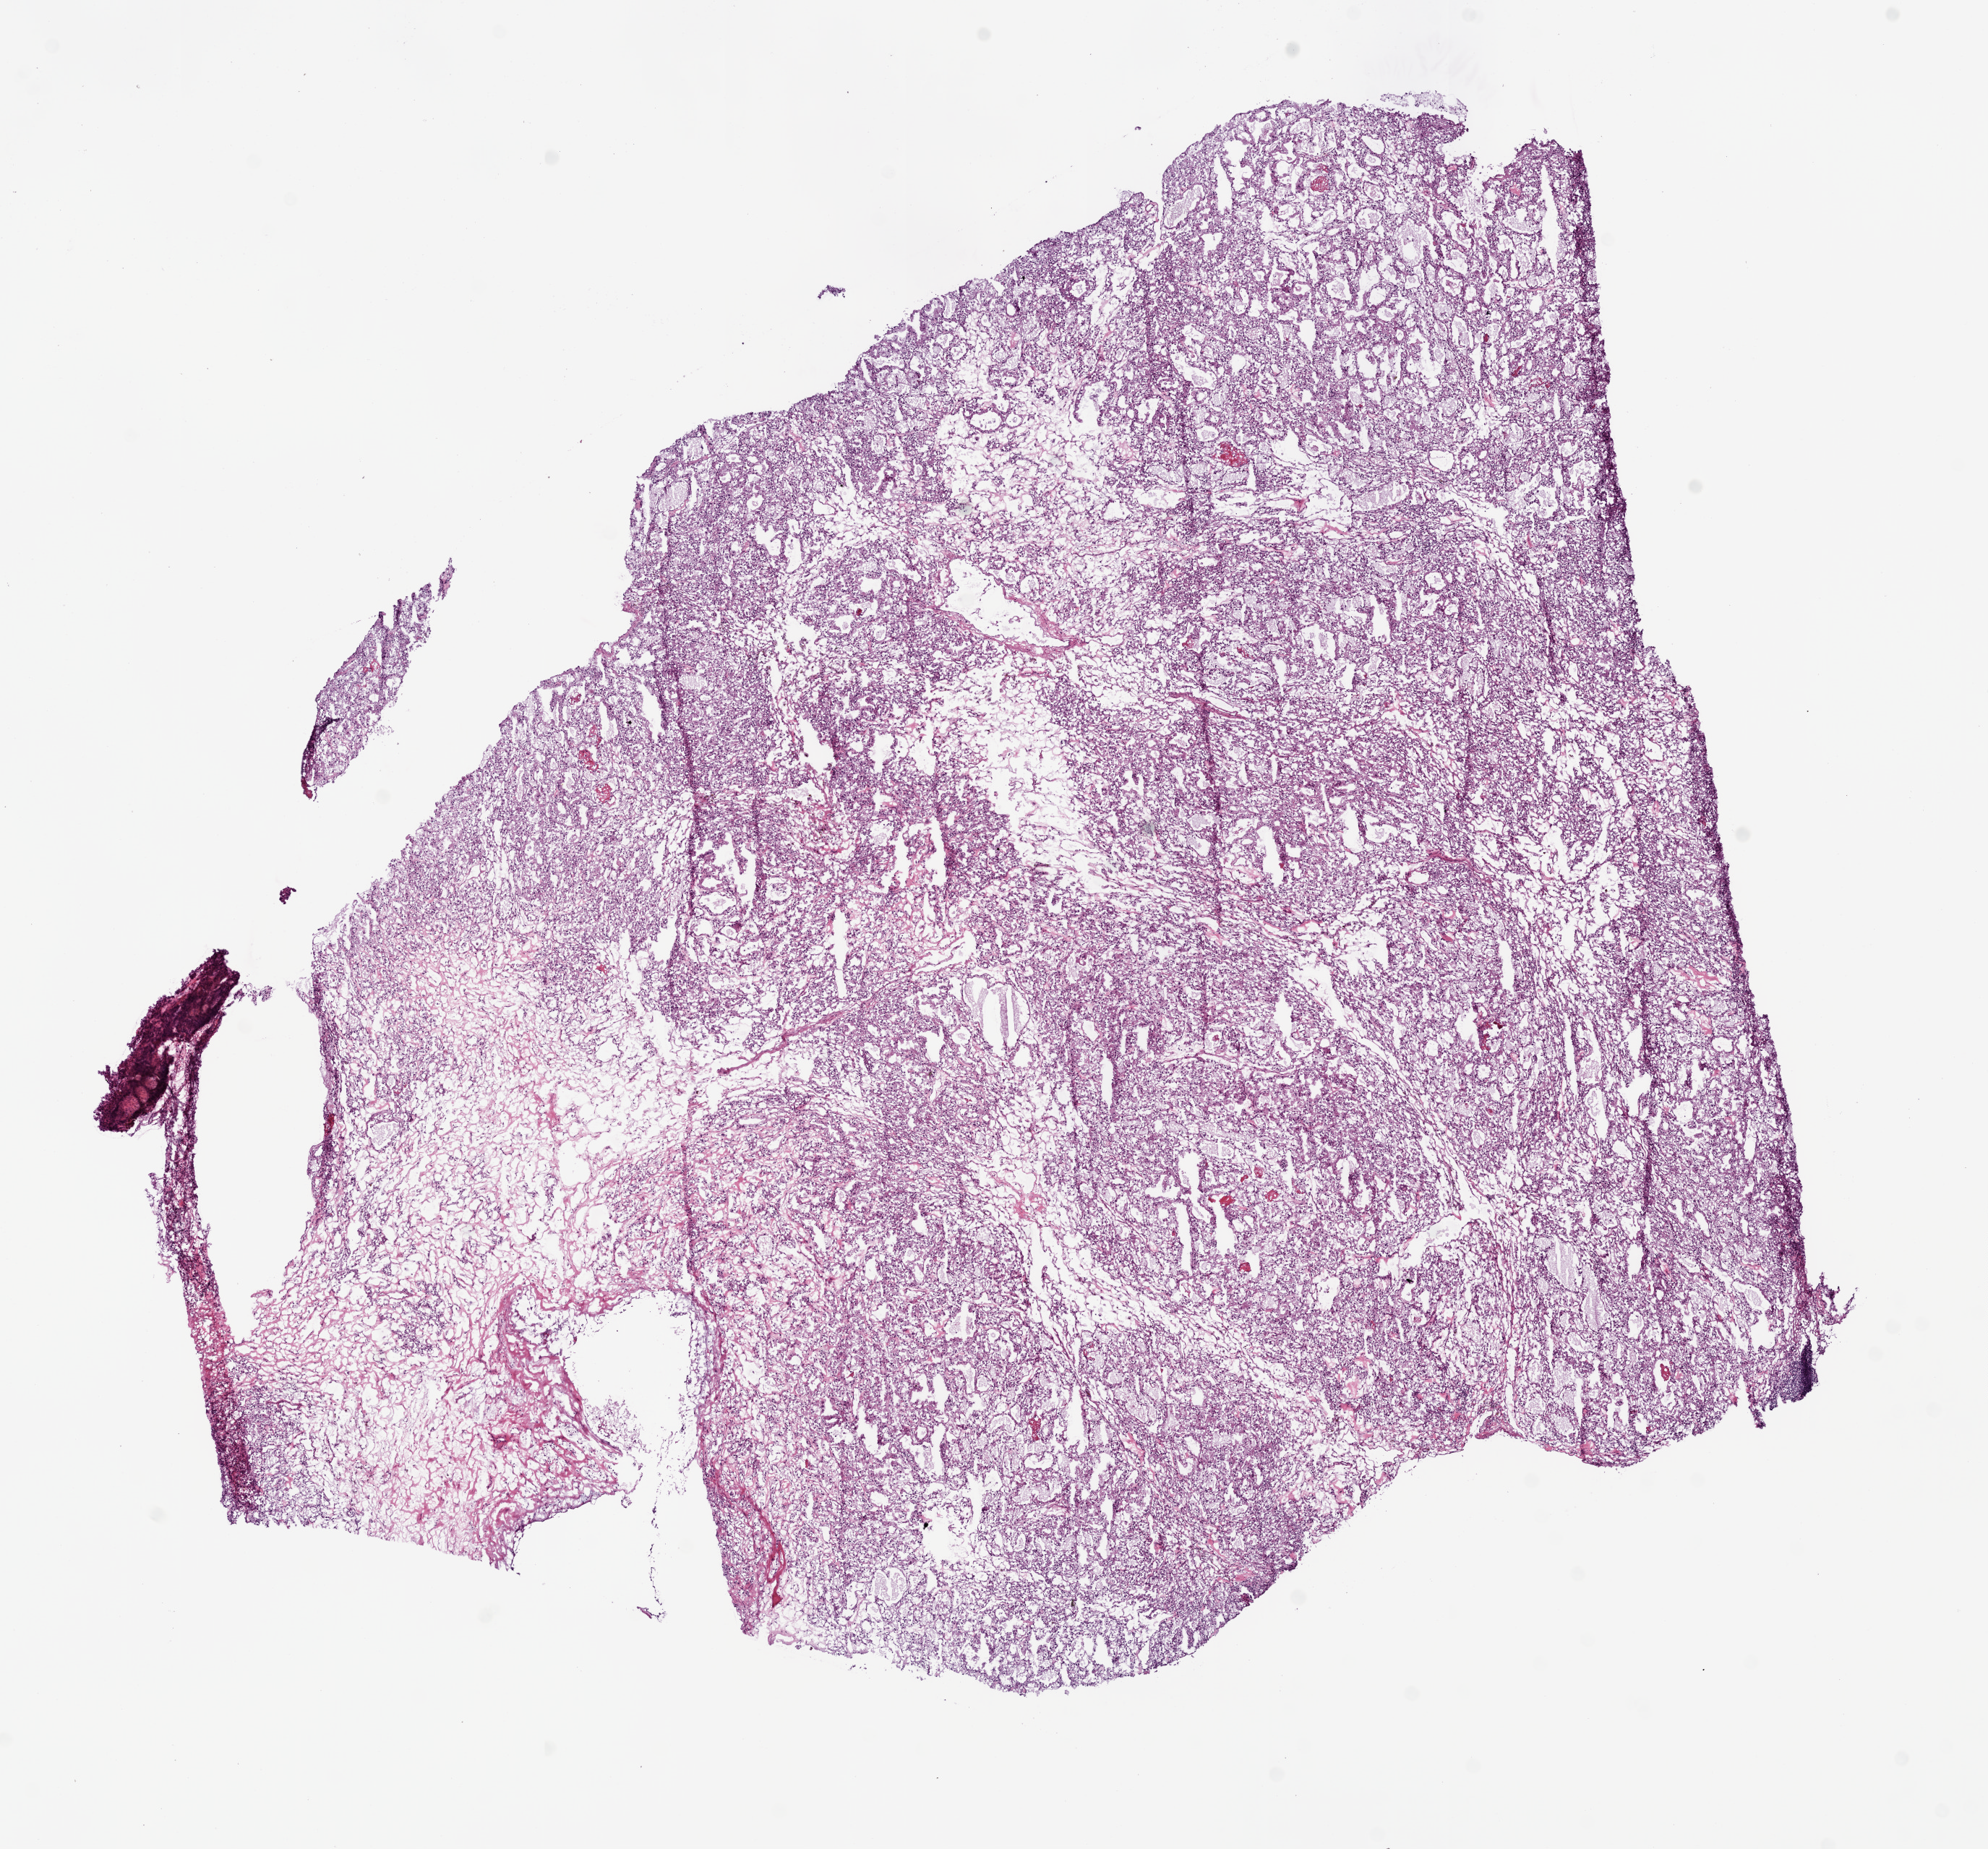
H&E whole-slide image, low-resolution overview of the scanned area, about 11.0 x 10.3 mm (acquisition: 20x scan), frozen section, kidney, primary tumour sample. Male, age 62 years at initial diagnosis.
Pathologic diagnosis: Clear cell adenocarcinoma, NOS.